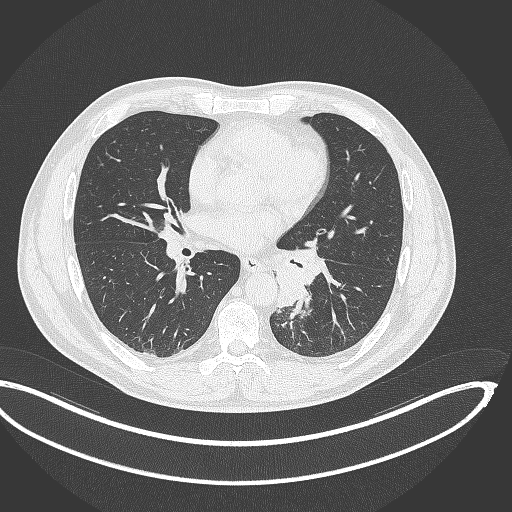
Chest CT, one axial slice; position 172 of 362 along the scan axis; reconstruction kernel B70f; 120 kVp; lung window (W 1500 / L -600 HU); 512 × 512 image matrix. Male patient, age 50 years. Case-level facts recorded for this patient, not image findings: clinical TNM (as recorded): T2a N3 M0.
Structures marked on this image (bounding box drawn by a radiologist):
- lung tumour (recorded histology: squamous cell carcinoma): bounding box <268,240,327,312> (left, top, right, bottom; pixels)